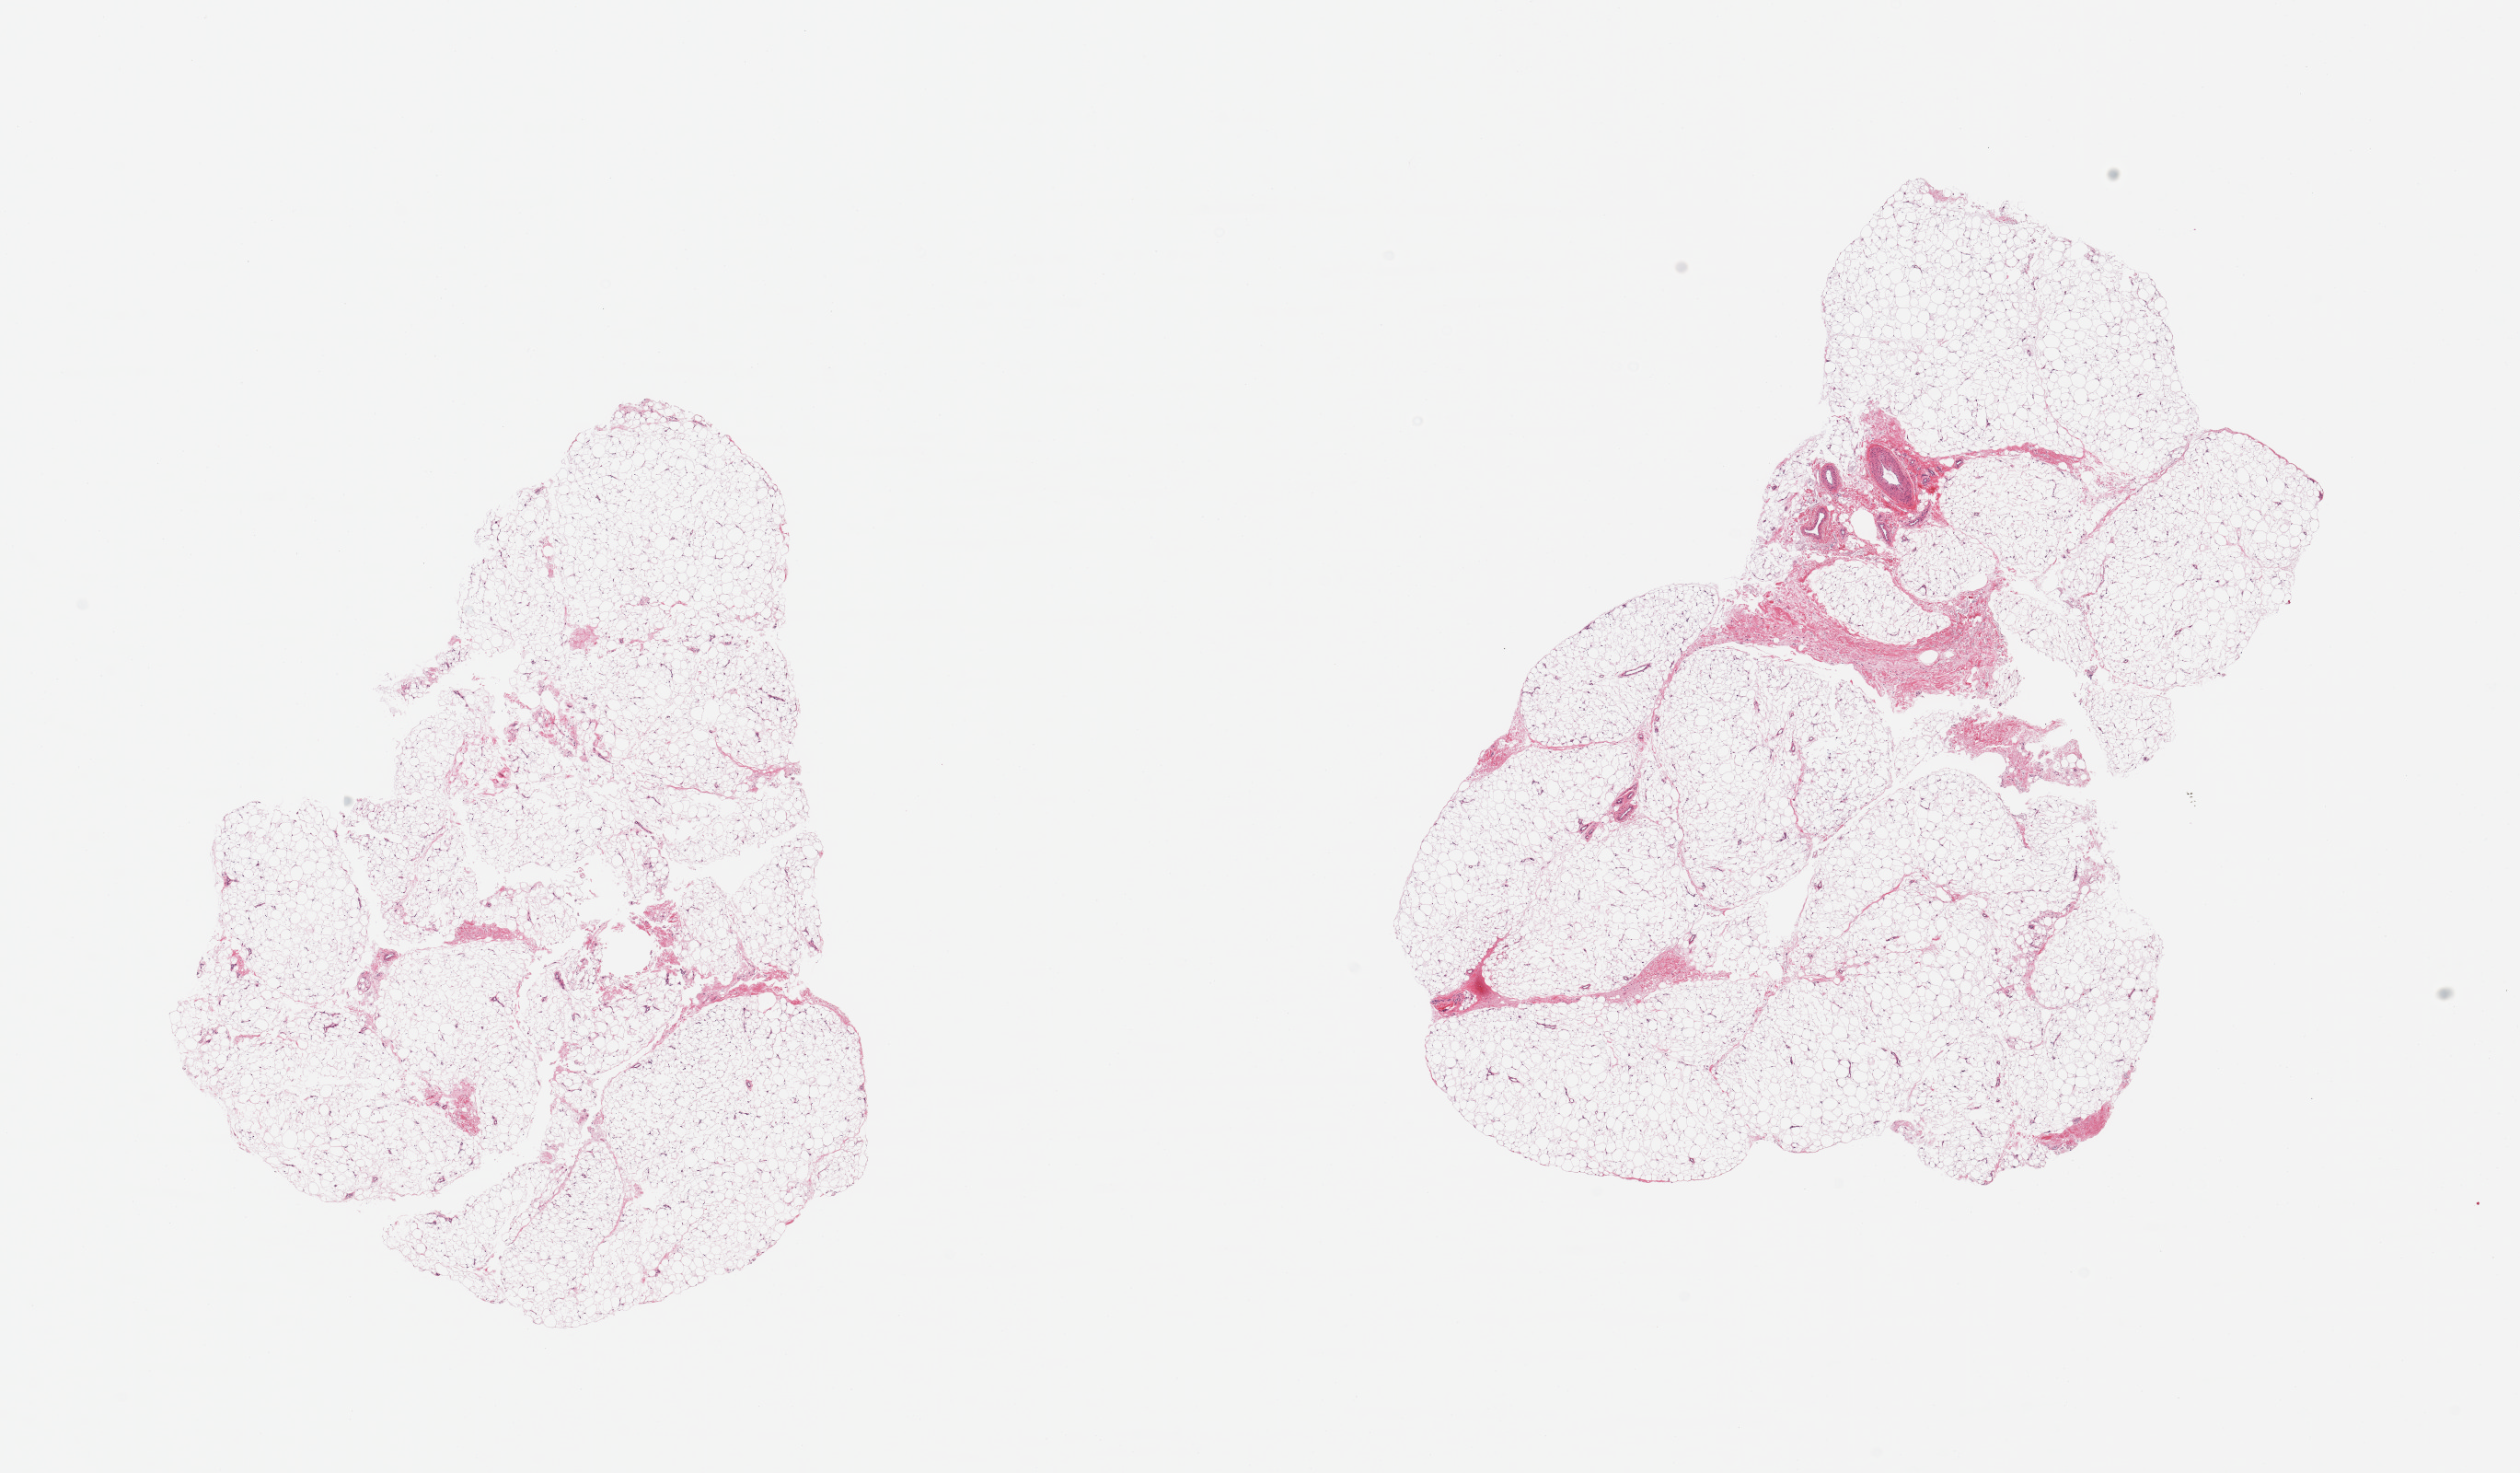
Digitized haematoxylin and eosin-stained section — a low-resolution overview of the entire scanned area, about 21.7 x 12.7 mm, PAXgene-fixed, paraffin-embedded tissue, section of adipose tissue (target tissue), tissue donor sample. Male donor.
* review note (as recorded): 2 pieces; mature fat, one piece includes about 10% fibrous tissue/vessels